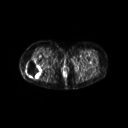
FDG PET of an extremity soft-tissue mass (from a PET/CT study), one axial slice. 3.27 mm slice thickness. 128 × 128 image matrix. Female patient, age 57 years. From the clinical record (not read from this slice): histological type: epithelioid sarcoma with vascular differentiation; site of the primary tumour: right buttock.
Outlined on this slice (expert contour drawn on MRI and transferred to this co-registered scan by the dataset authors):
- gross tumour volume (mass): bounding box [x1, y1, x2, y2] px = [25, 59, 42, 77]